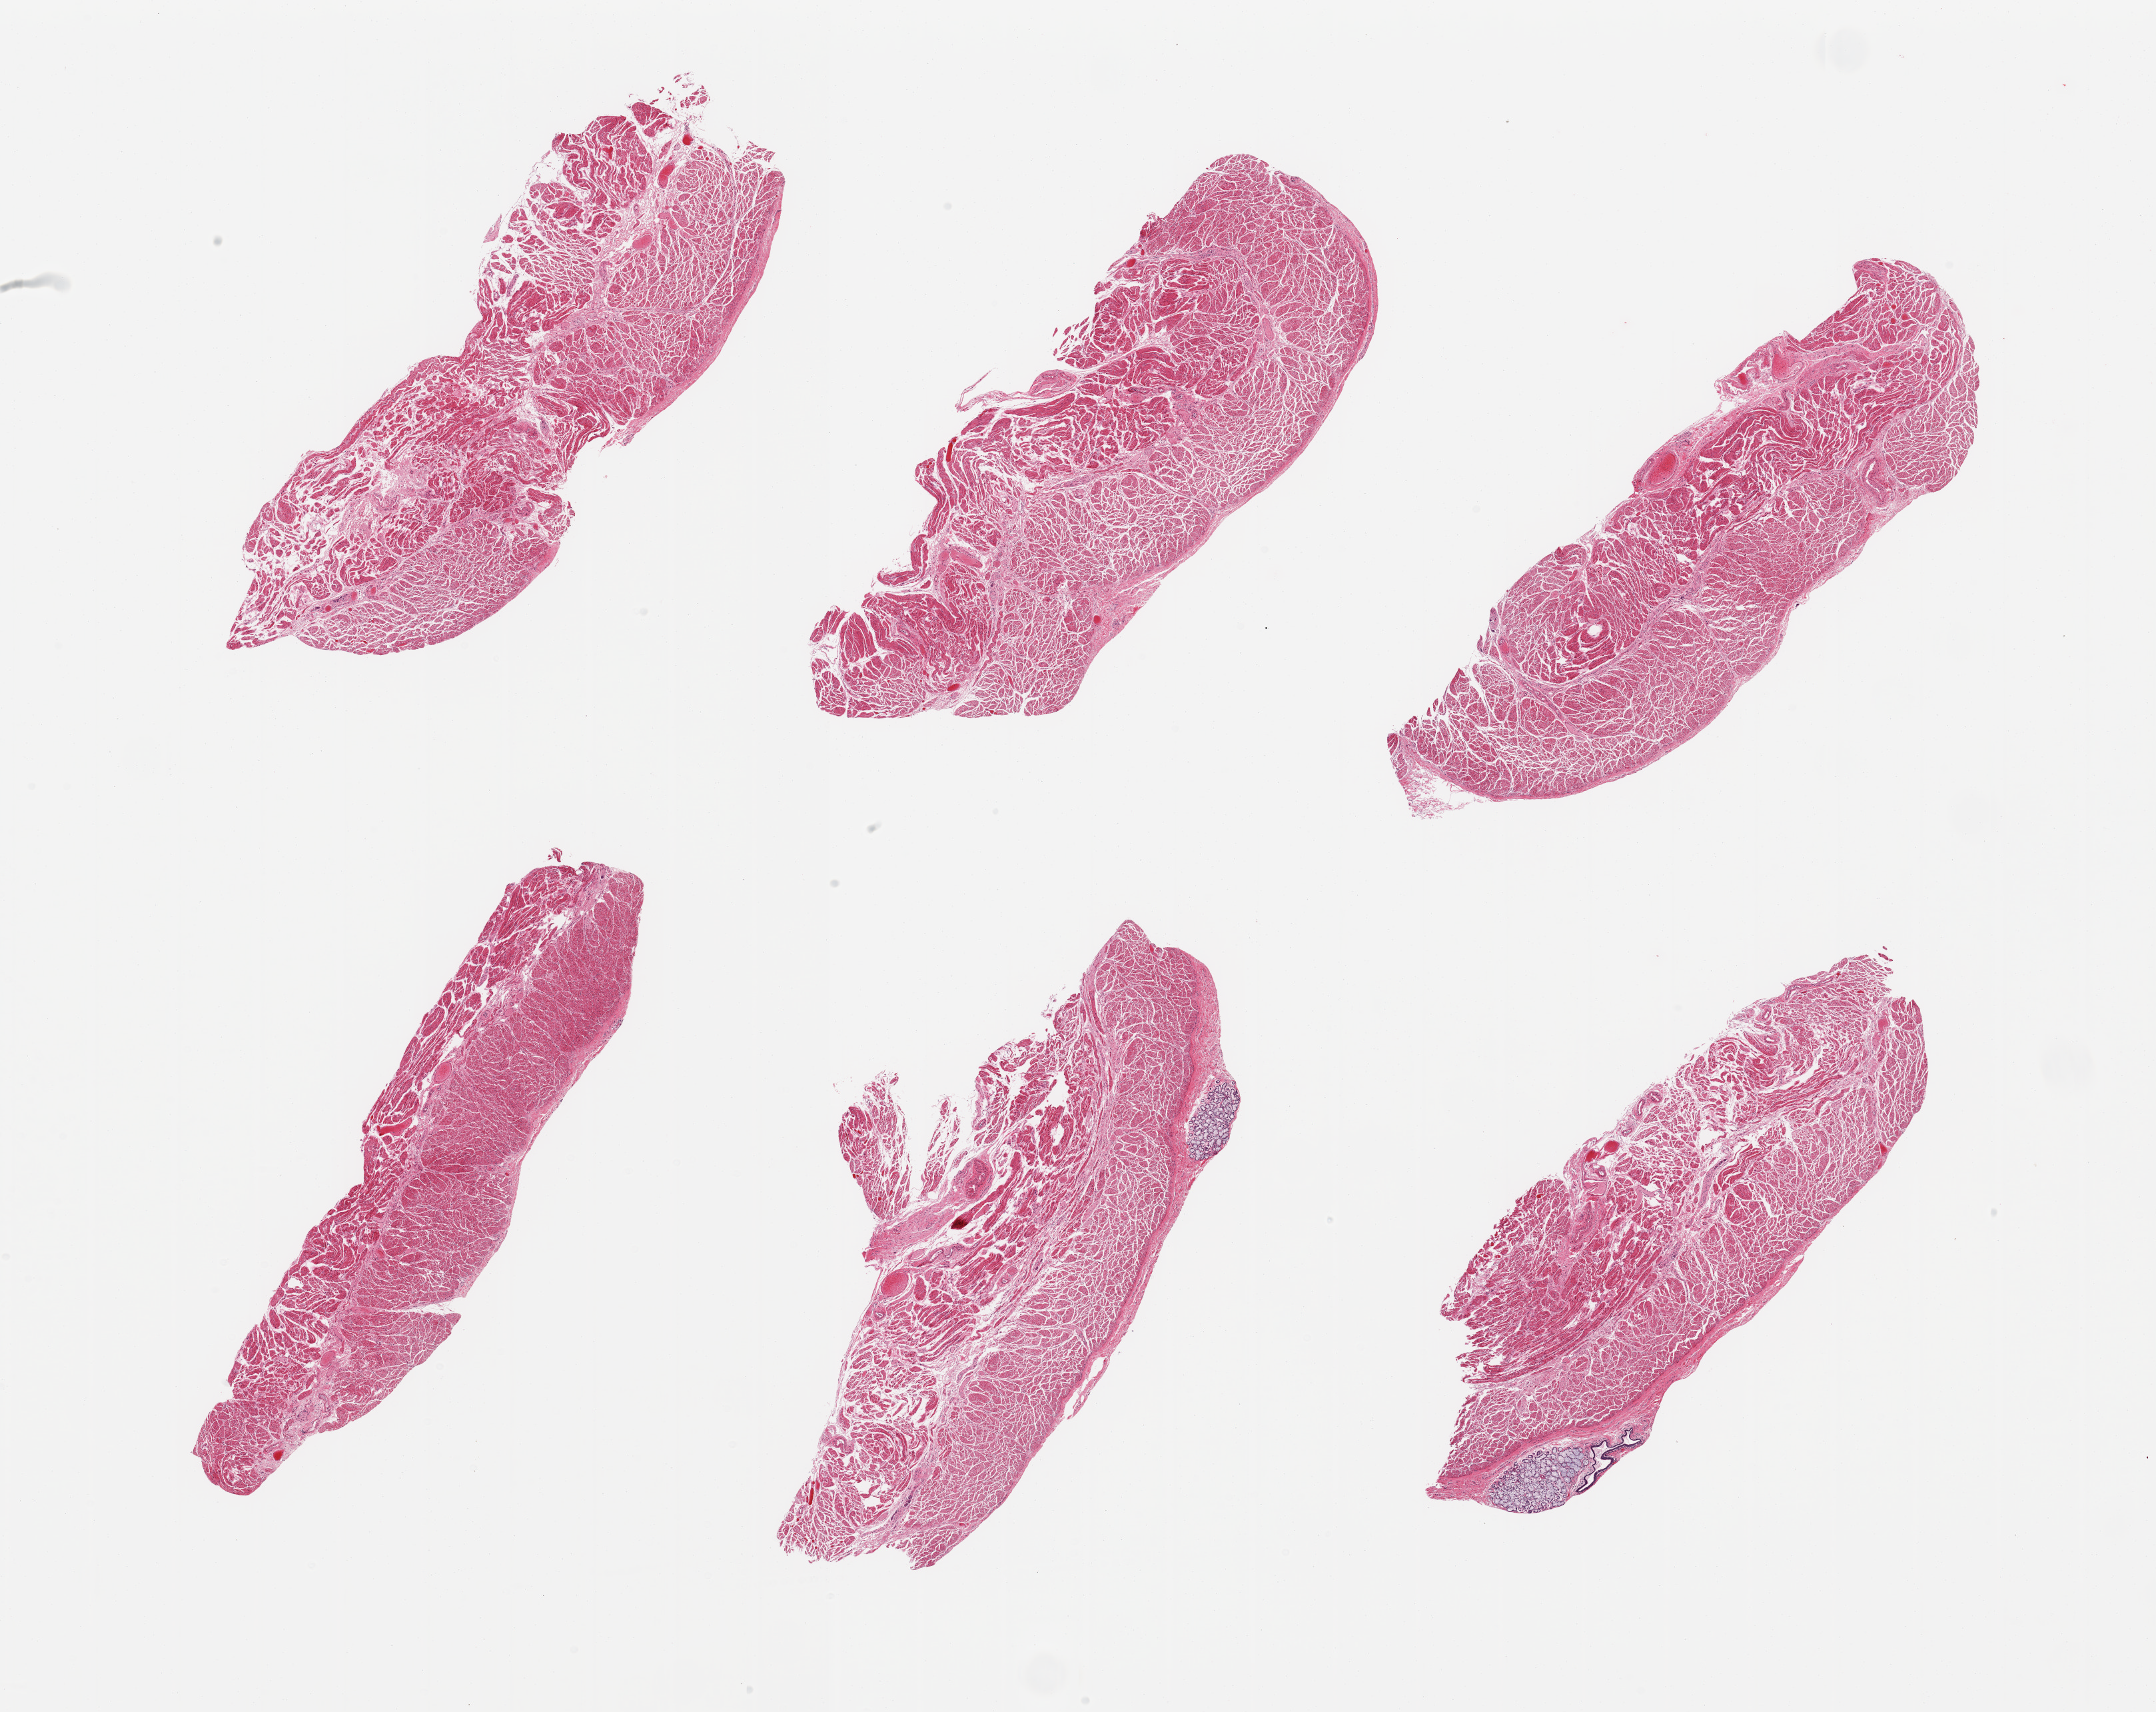
Hematoxylin and eosin (H&E) whole-slide image — whole scanned area (about 25.6 x 20.3 mm, acquisition: 20x scan) shown as a low-resolution overview, PAXgene-fixed paraffin-embedded (PFPE) section, target tissue: esophageal muscle, donor tissue sample. Donor: female.
Pathologist's review note for this sample: 6 pieces, confirmed target muscularis.